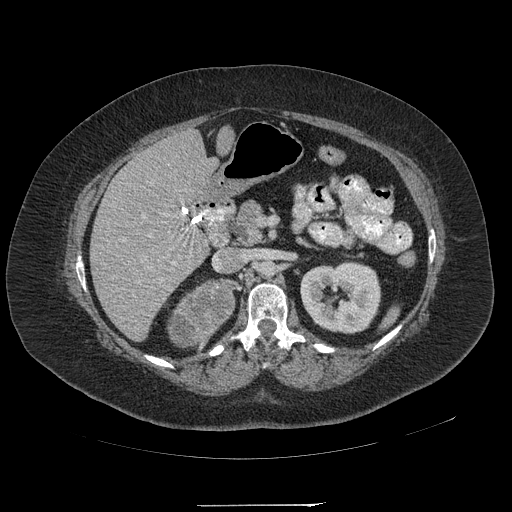
Contrast-enhanced abdominal CT, one axial slice; slice 115 of 217 in the series (ordered by position); reconstruction kernel STANDARD; 120 kVp; intravenous contrast given; soft-tissue window (W 400 / L 40 HU); 512 × 512 image matrix, field of view 453 × 453 mm. Patient: female, 55 years. Case-level facts recorded for this patient, not image findings: diagnosis: adrenocortical carcinoma; tumour side: right adrenal; tumour size at pathology: 11 cm; Ki-67 index: 20 %; stage (as recorded): 2.
Outlined on this slice (semi-automatic segmentation, software-assisted and operator-edited):
- mass: box from (x=169, y=282) to (x=233, y=348) px